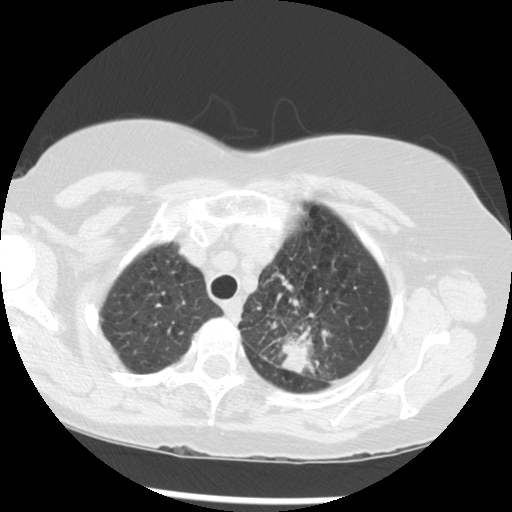
Low-dose screening chest CT, one axial slice; slice 237 of 283 in the series (ordered by position); 120 kVp; lung window (W 1500 / L -600 HU); 512 × 512 image matrix, field of view 330 × 330 mm.
Outlined on this slice (outlined manually by an expert reader):
- lesion 1 (tumor, upper lobe of left lung): bounding box <281,328,316,374> (left, top, right, bottom; pixels)